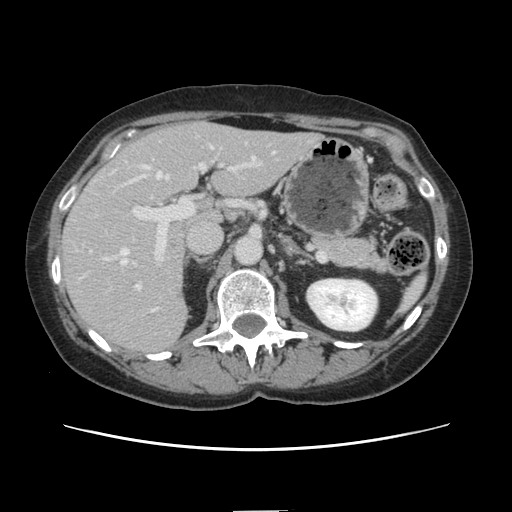
Contrast-enhanced abdominal CT, one axial slice; slice 79 of 141 in the series (ordered by position); 120 kVp; soft-tissue window (W 400 / L 40 HU); 2.5 mm slice thickness; 512 × 512 image matrix, field of view 350 × 350 mm. Female patient, age 63 years. Case-level facts recorded for this patient, not image findings: diagnosis: colorectal cancer liver metastases, imaged before liver resection; multiple liver metastases: yes; largest metastasis: 3.2 cm; disease in both lobes: yes.
Structures marked on this image (expert manual segmentation):
- hepatic veins: box from (x=83, y=158) to (x=257, y=277) px
- liver: (x=61, y=123)–(x=317, y=354)
- planned liver remnant (the part of the liver to remain after resection): (x=175, y=123)–(x=317, y=221)
- portal vein (with intrahepatic branches): (x=132, y=153)–(x=252, y=292)
- liver metastasis: (x=173, y=292)–(x=184, y=302)
- liver metastasis: (x=147, y=311)–(x=159, y=323)